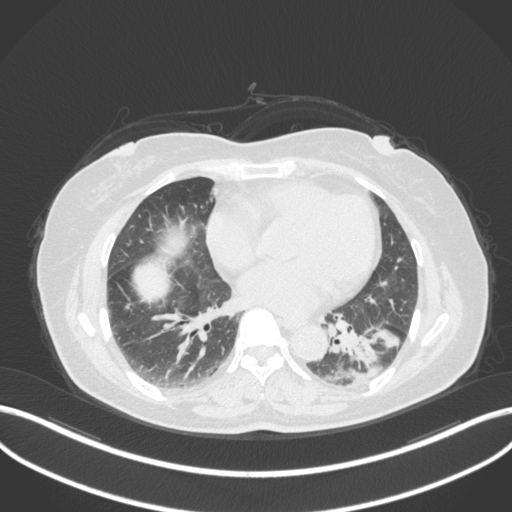
Chest CT, one axial slice; reconstruction kernel B31f; lung window (W 1500 / L -600 HU); 512 × 512 image matrix. Patient: female, 59 years. From the clinical record (not read from this slice): clinical TNM (as recorded): T2a N0 M0.
Outlined on this slice (bounding box drawn by a radiologist):
- lung tumour (recorded histology: adenocarcinoma): bounding box <324,321,401,389> (left, top, right, bottom; pixels)